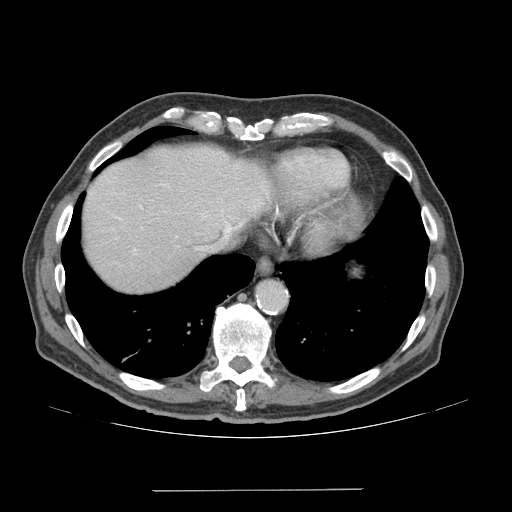
Contrast-enhanced abdominal CT (liver protocol), one axial slice. Slice 61 of 77 in the series (ordered by position). Reconstruction kernel STANDARD. 140 kVp. Soft-tissue window (W 400 / L 40 HU). 2.5 mm slice thickness. 512 × 512 image matrix, field of view 400 × 400 mm. Case-level facts recorded for this patient, not image findings: diagnosis: hepatocellular carcinoma (patient treated with transarterial chemoembolisation; whether this scan precedes or follows treatment is not stated here); TNM stage (as recorded): Stage-IVA; Child-Pugh class: A.
Annotated regions visible in this slice (semi-automatic segmentation, software-assisted and operator-edited):
- abdominal aorta: box from (x=257, y=282) to (x=287, y=310) px
- liver parenchyma outside the tumour (the mass and vessels are separate outlines, so this box may not span the whole liver): (x=82, y=146)–(x=272, y=292)
- liver vessels: (x=115, y=184)–(x=256, y=251)